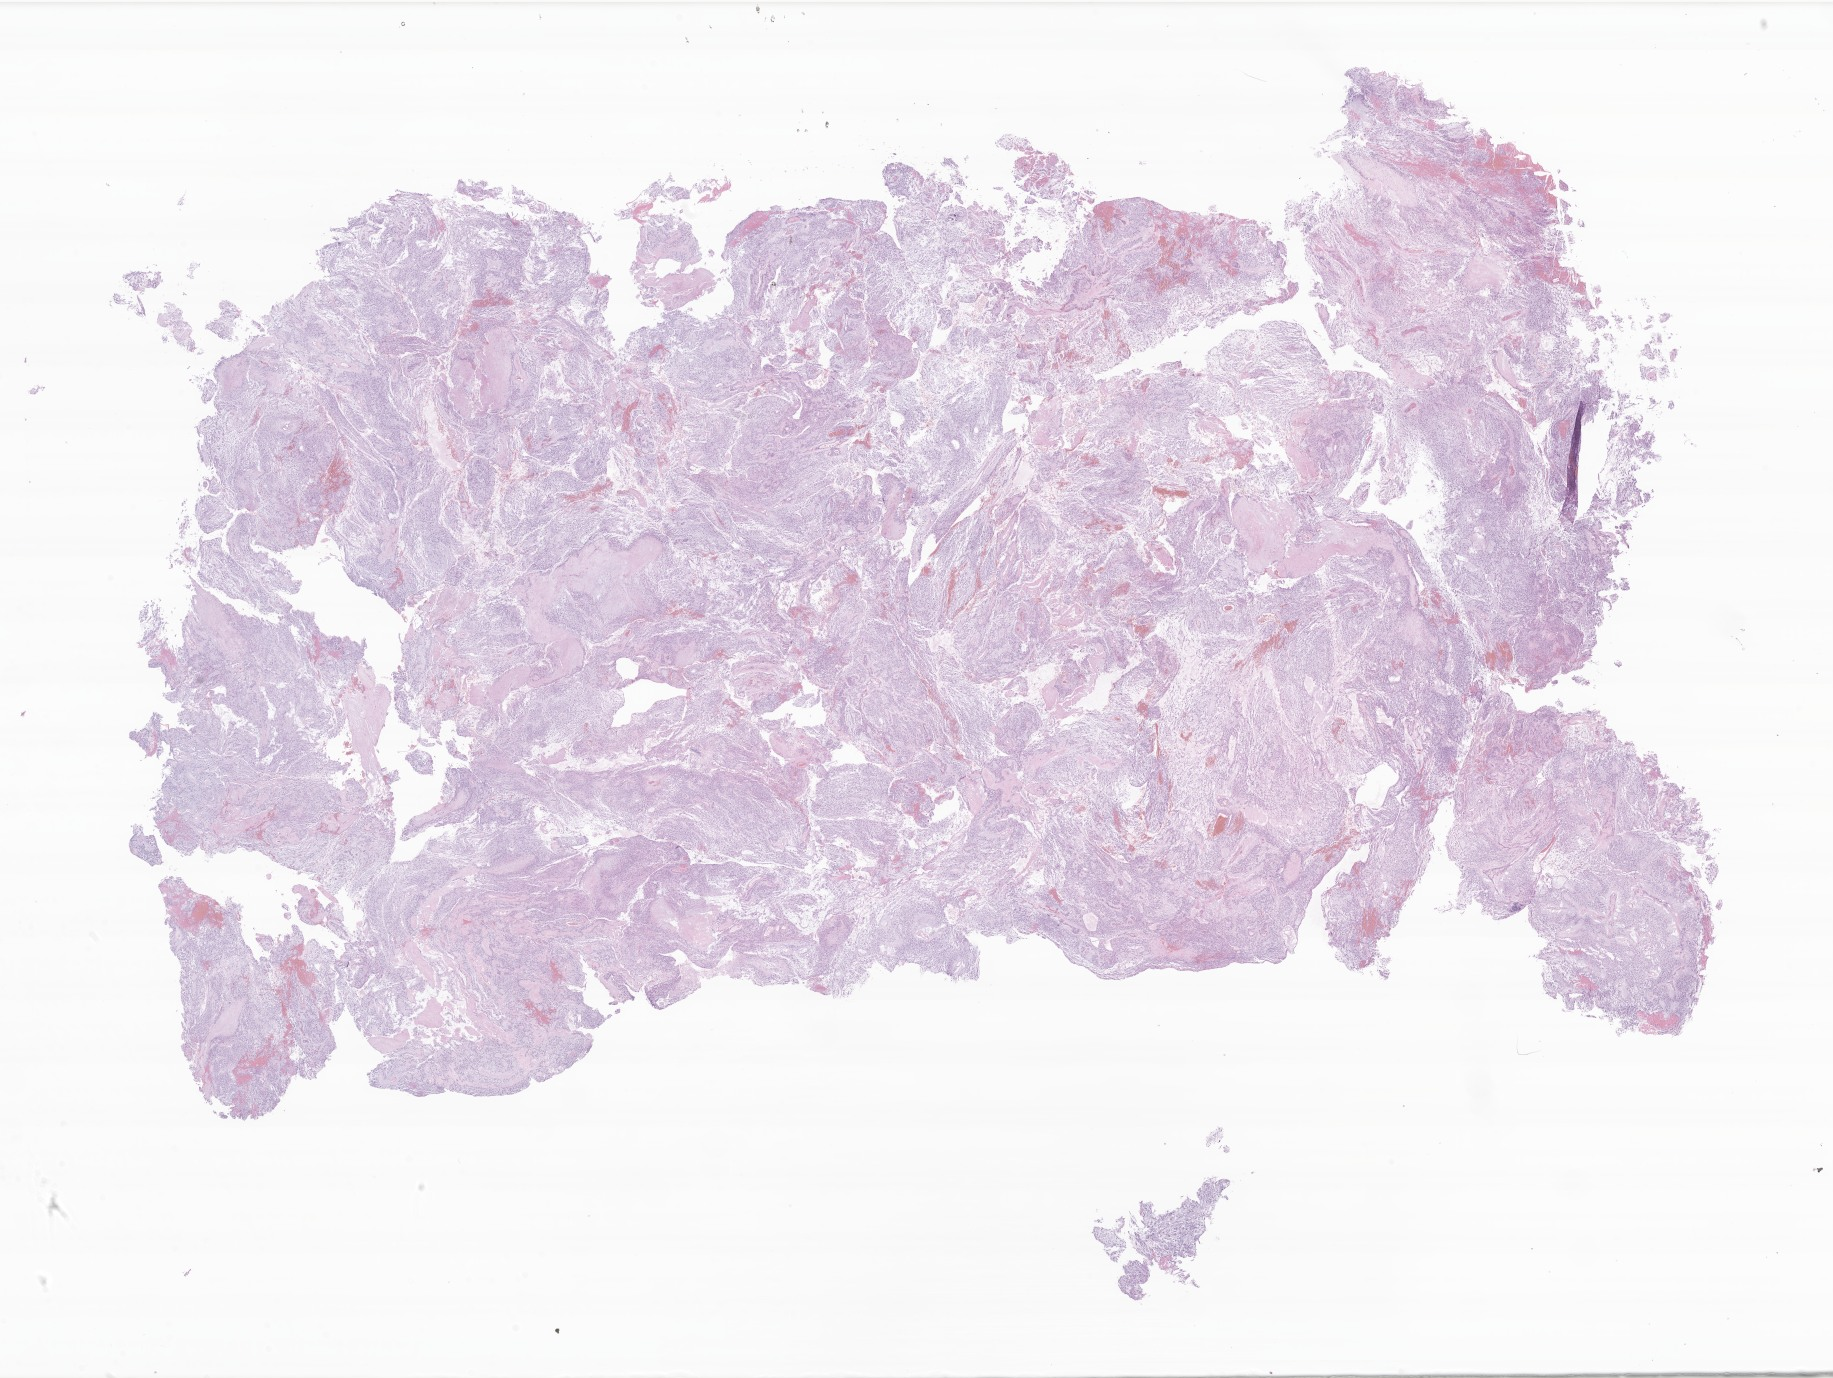
Hematoxylin and eosin (H&E) whole-slide image of tumor tissue from the spinal cord, low-resolution overview of the scanned area, about 30.9 x 23.2 mm; formalin-fixed paraffin-embedded section. Patient: male, age 175 months (14 years 7 months).
• diagnosis (ICD-O-3 morphology term): Myxopapillary ependymoma